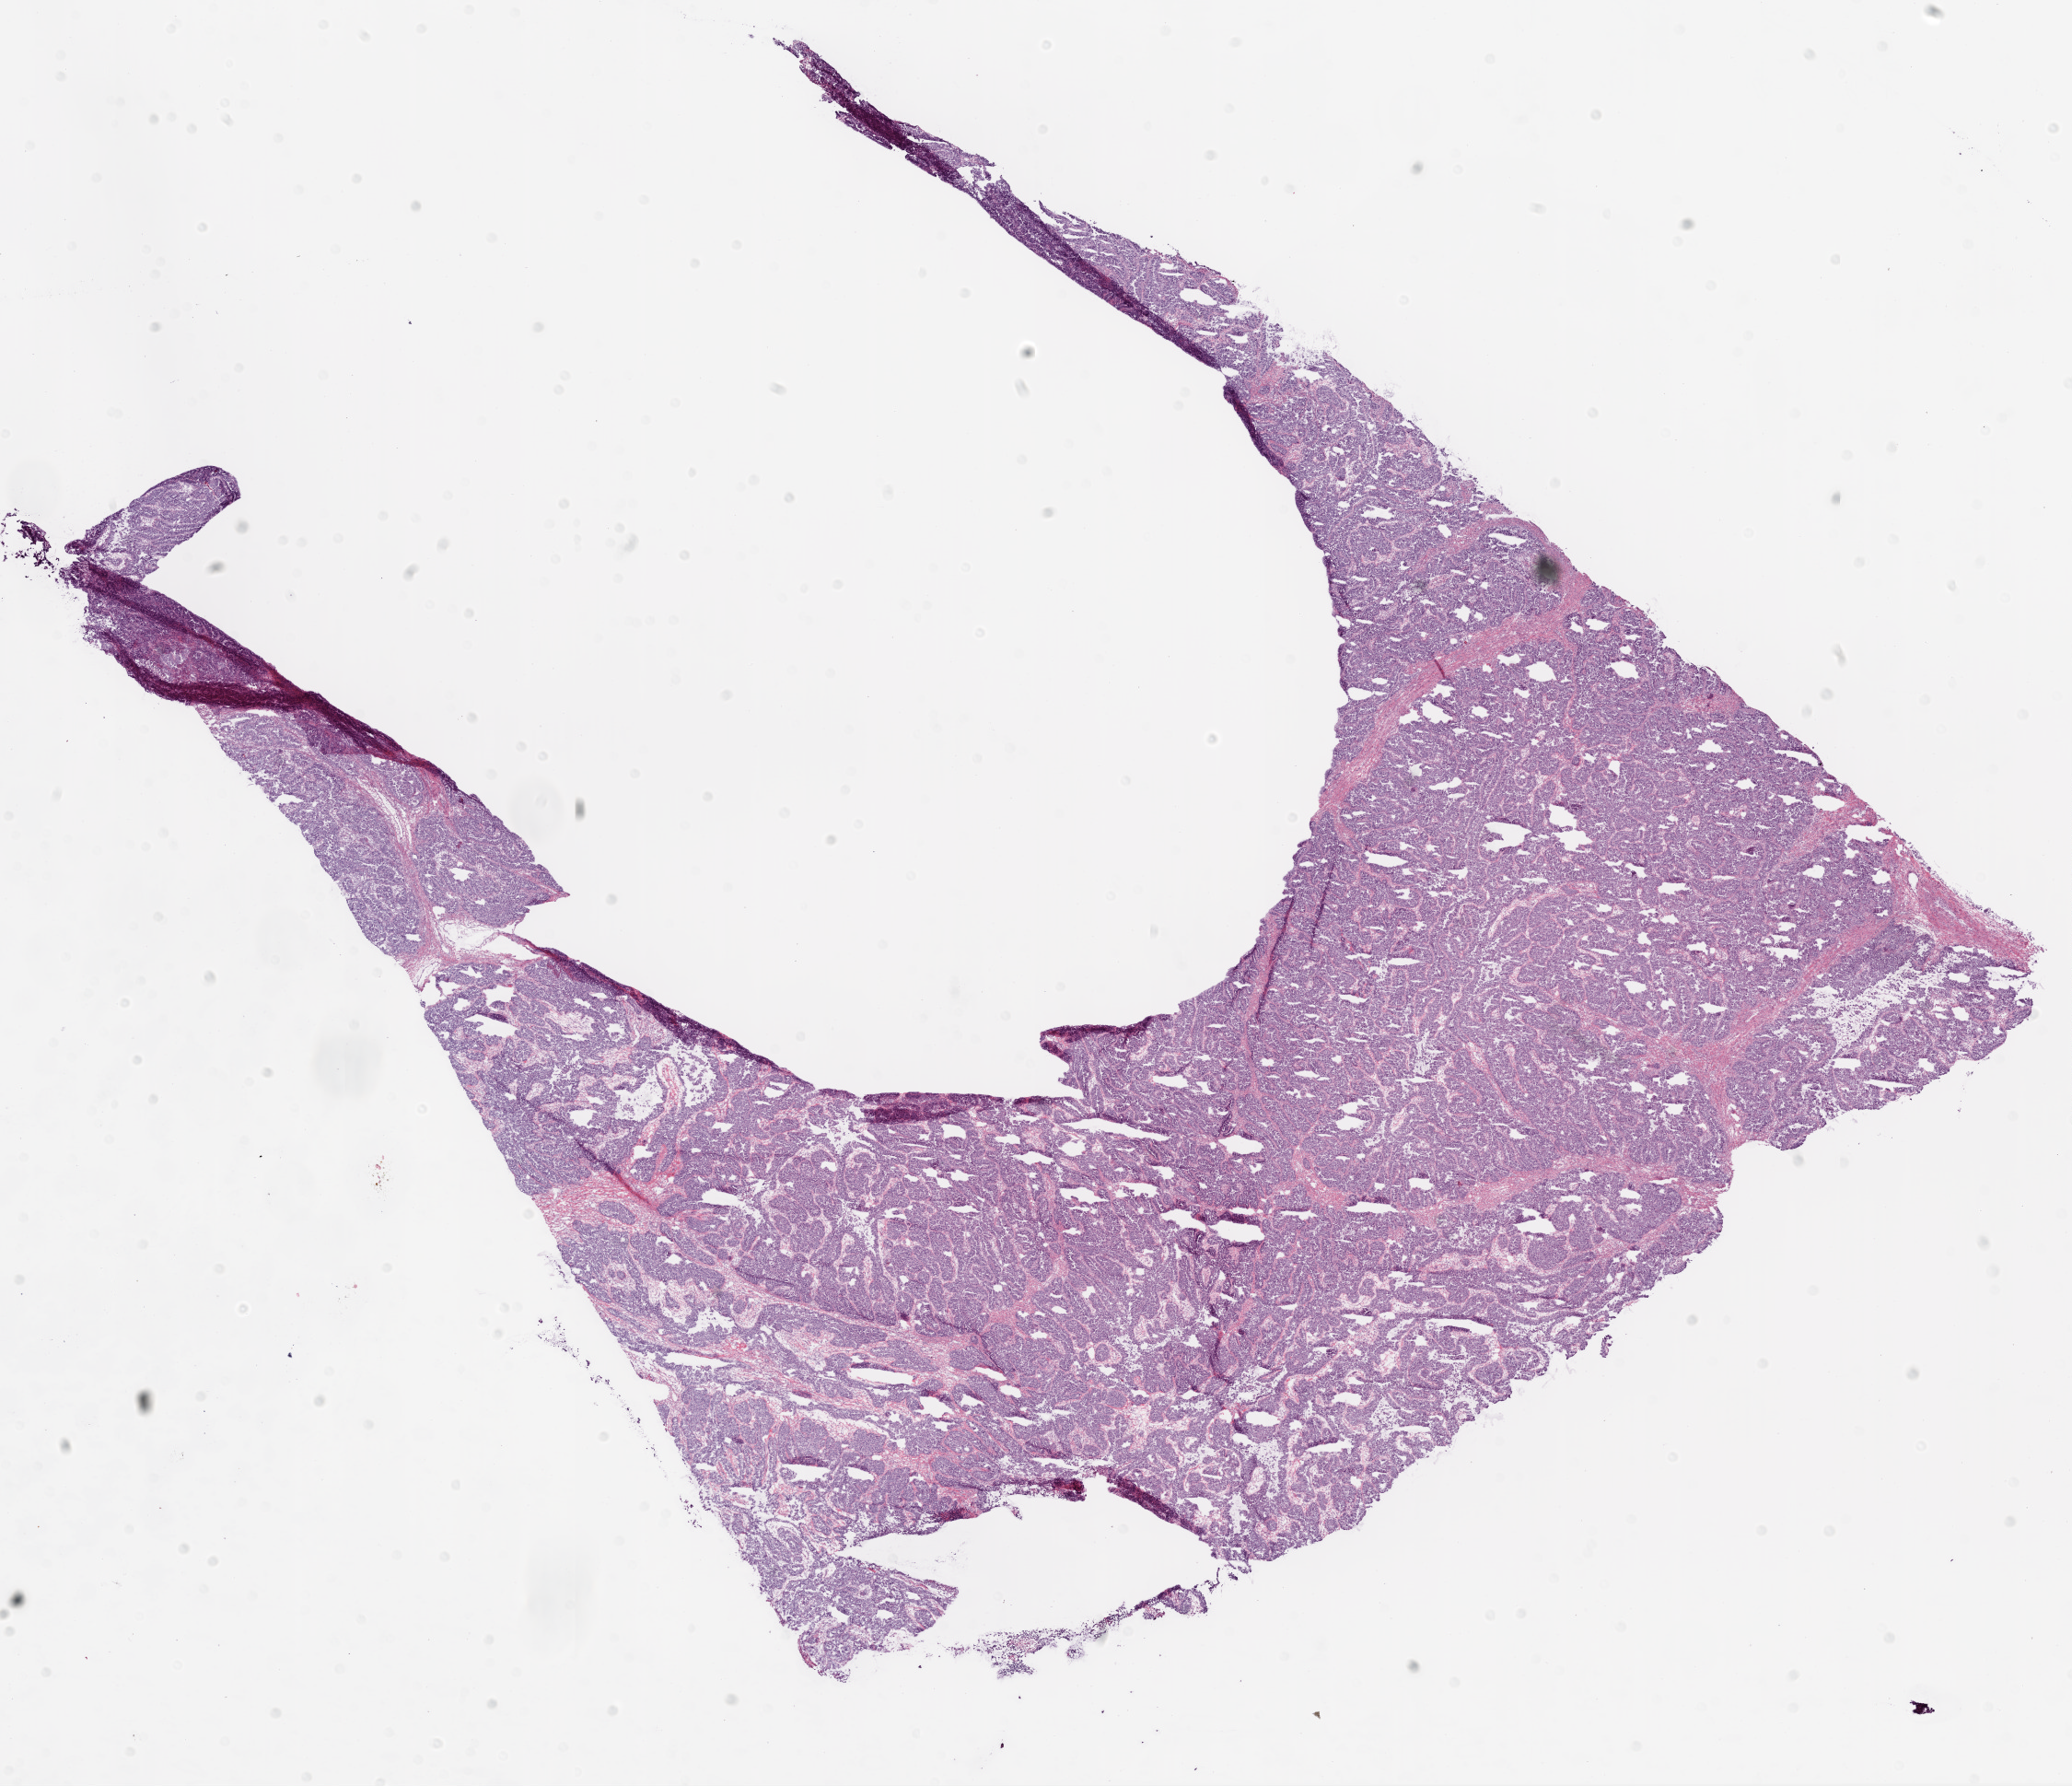
Digitized H&E tissue section (whole slide), shown as a low-resolution overview of the whole scanned area (about 18.1 x 15.6 mm, acquisition: 20x scan). Frozen section from the bottom of the tissue portion. Primary tumour sample from the ovary. Female, age 81 years at initial diagnosis. Histologic grade: G3 (poorly differentiated). Pathologist review of this section (percent, as recorded): tumour cells 95%, tumour nuclei 95%, normal cells 0%, stromal cells 5%, necrosis 0%.
Histologic diagnosis: Serous cystadenocarcinoma, NOS. FIGO stage: IIIC.